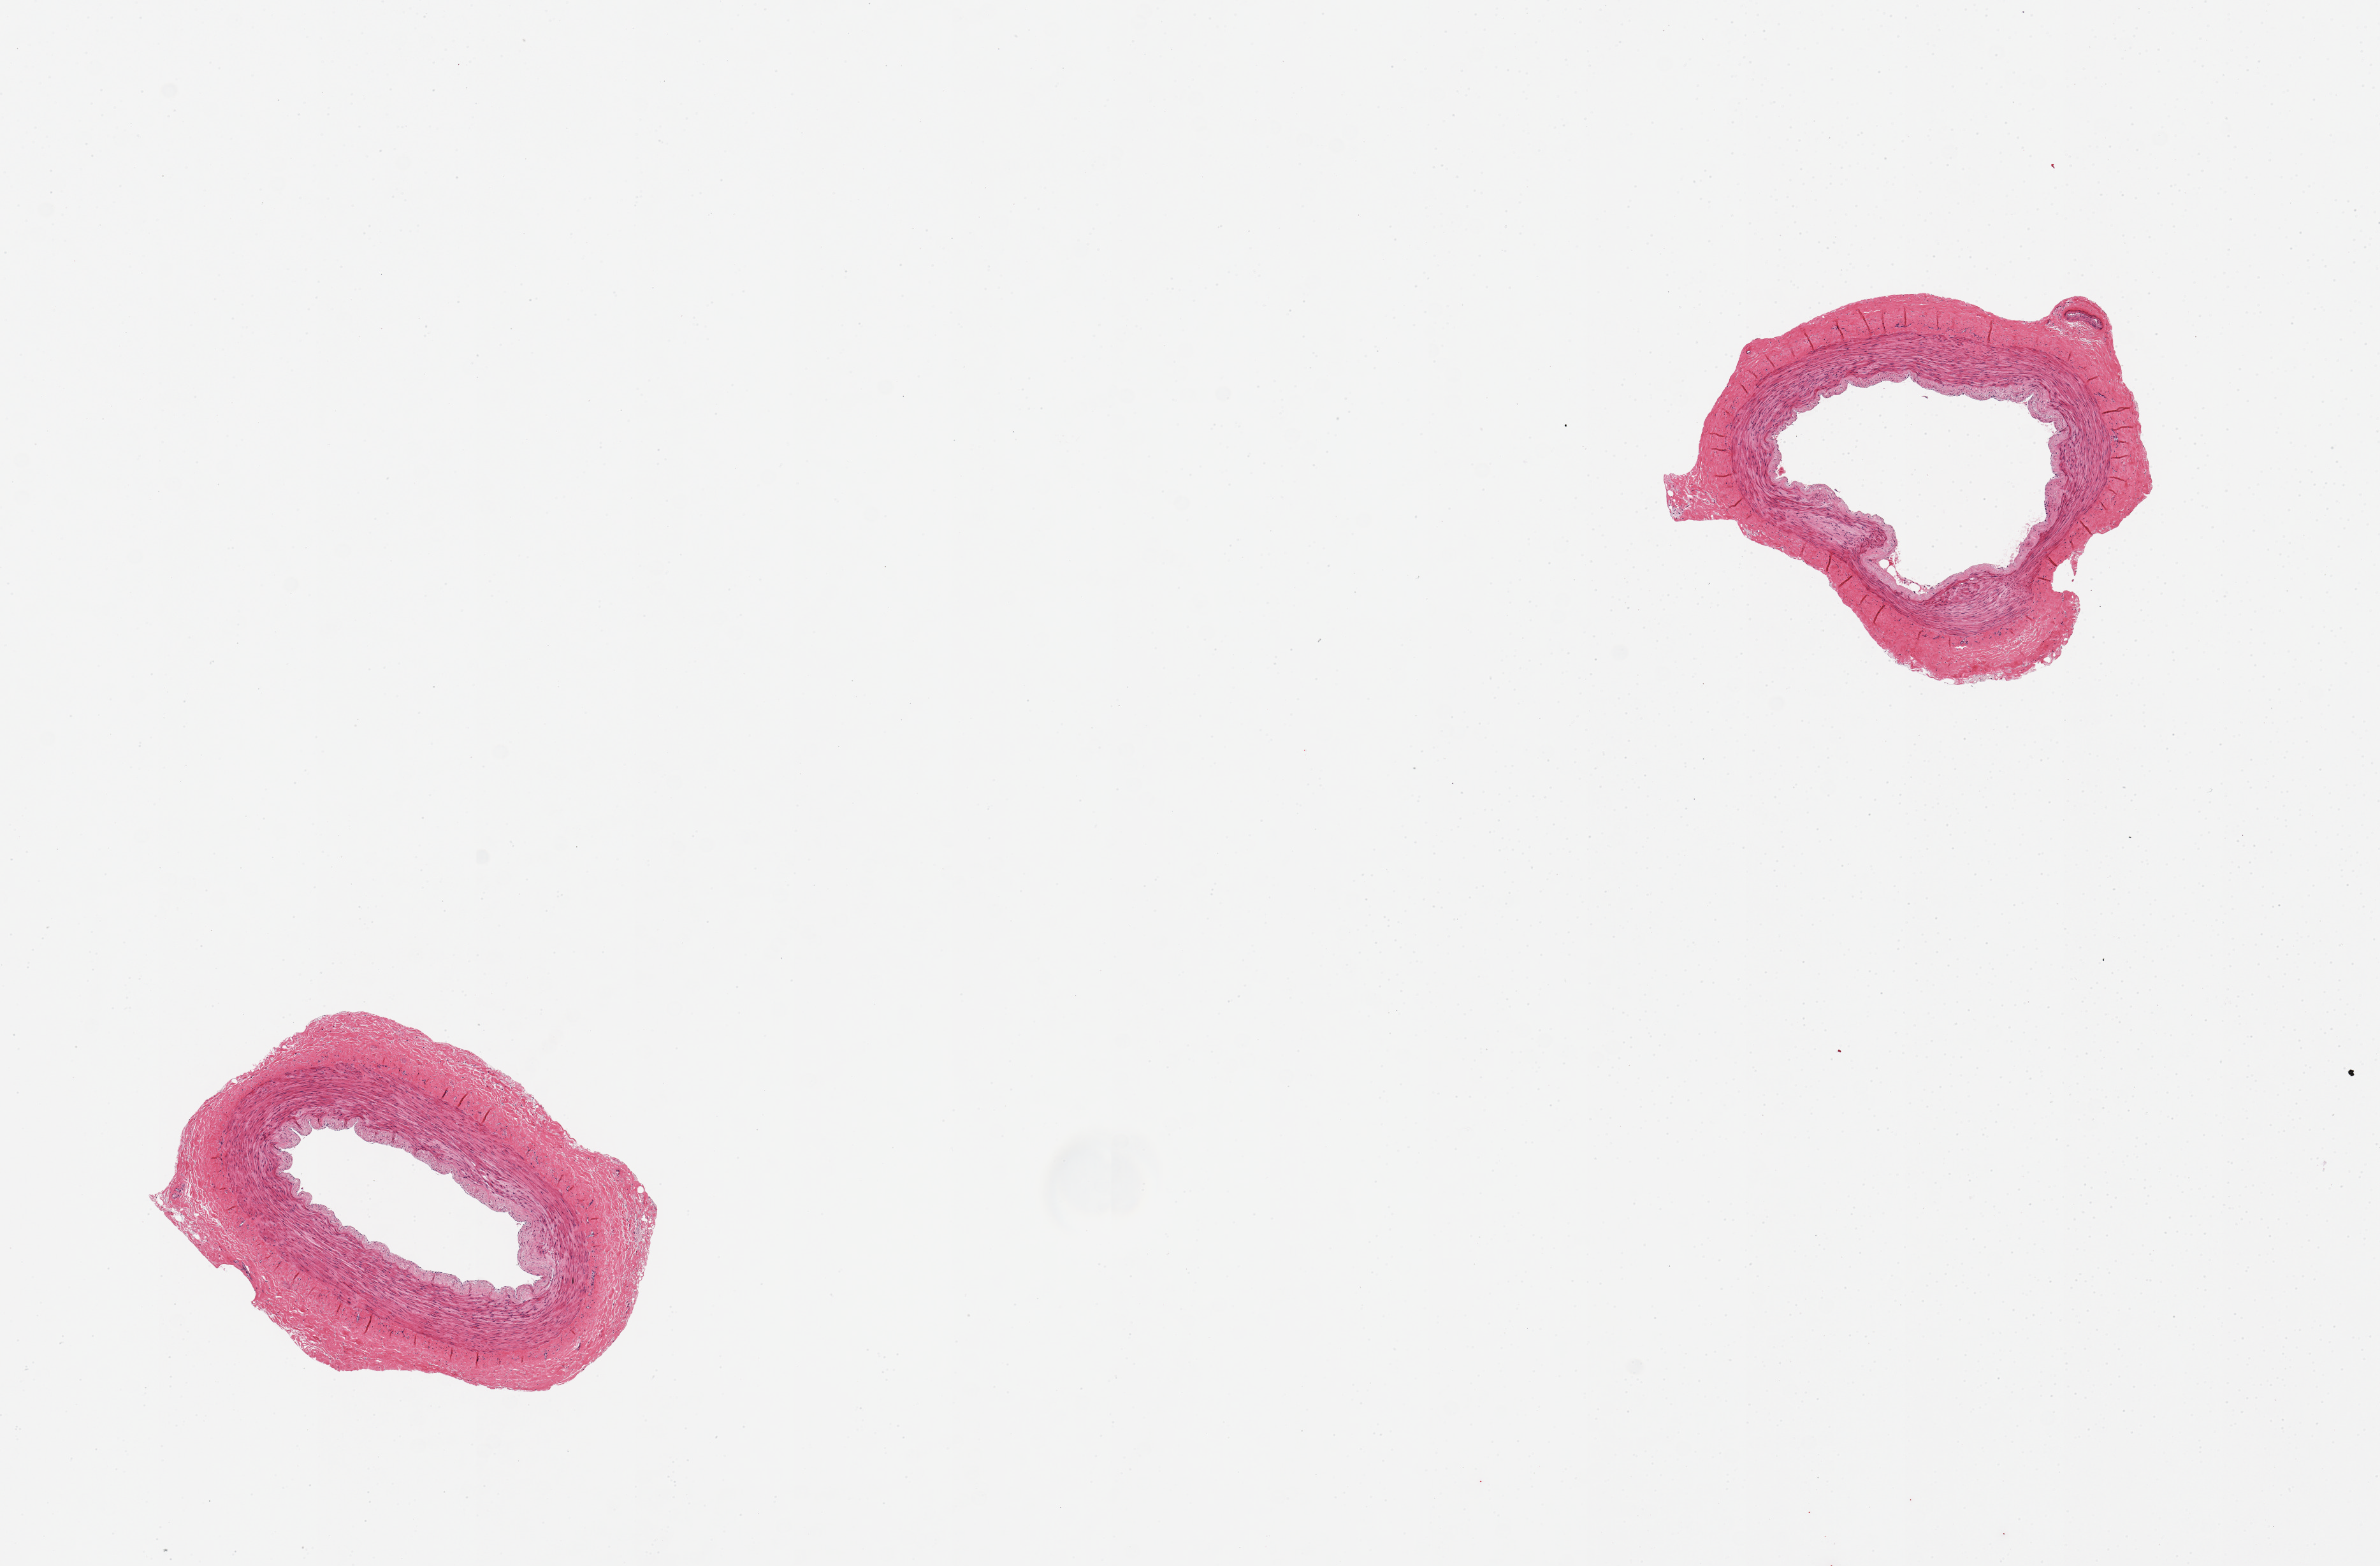
H&E whole-slide image, a low-resolution overview of the entire scanned area, about 14.8 x 9.7 mm (slide scanned at 20x); PAXgene-fixed, paraffin-embedded tissue; section of tibial artery (target tissue); tissue donor sample. Female donor.
• review note (as recorded): 2 pieces, perfect clean specimens, not atherosis noted